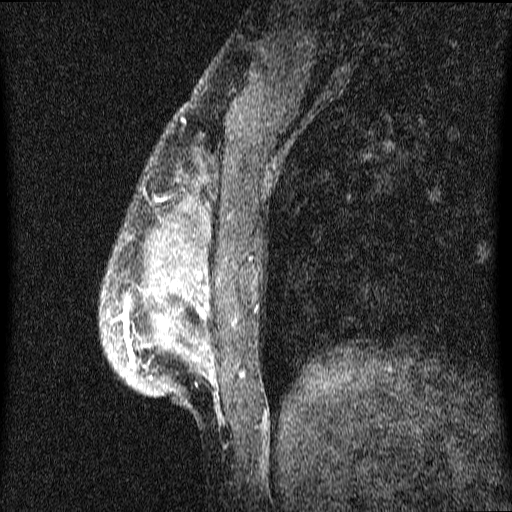
Breast MRI (dynamic contrast-enhanced), one sagittal slice. Slice 17 of 64 in the series (ordered by position). Dynamic contrast-enhanced series, image 2 of 4 at this slice position (ordered by acquisition). 1.5 T. TE 4.2 ms, TR 9.1 ms. 2 mm slice thickness. 512 × 512 image matrix. Patient: female, 33 years.
Structures marked on this image (semi-automatic segmentation, software-assisted and operator-edited):
- analysis volume of interest (the breast-tissue region the enhancement analysis was run in; not a lesion): bounding box (x1, y1, x2, y2) in pixels: (101, 151, 266, 427)
- tumour enhancement mask (voxels above the 70 % enhancement threshold inside the analysis volume of interest): (118, 273, 214, 381)